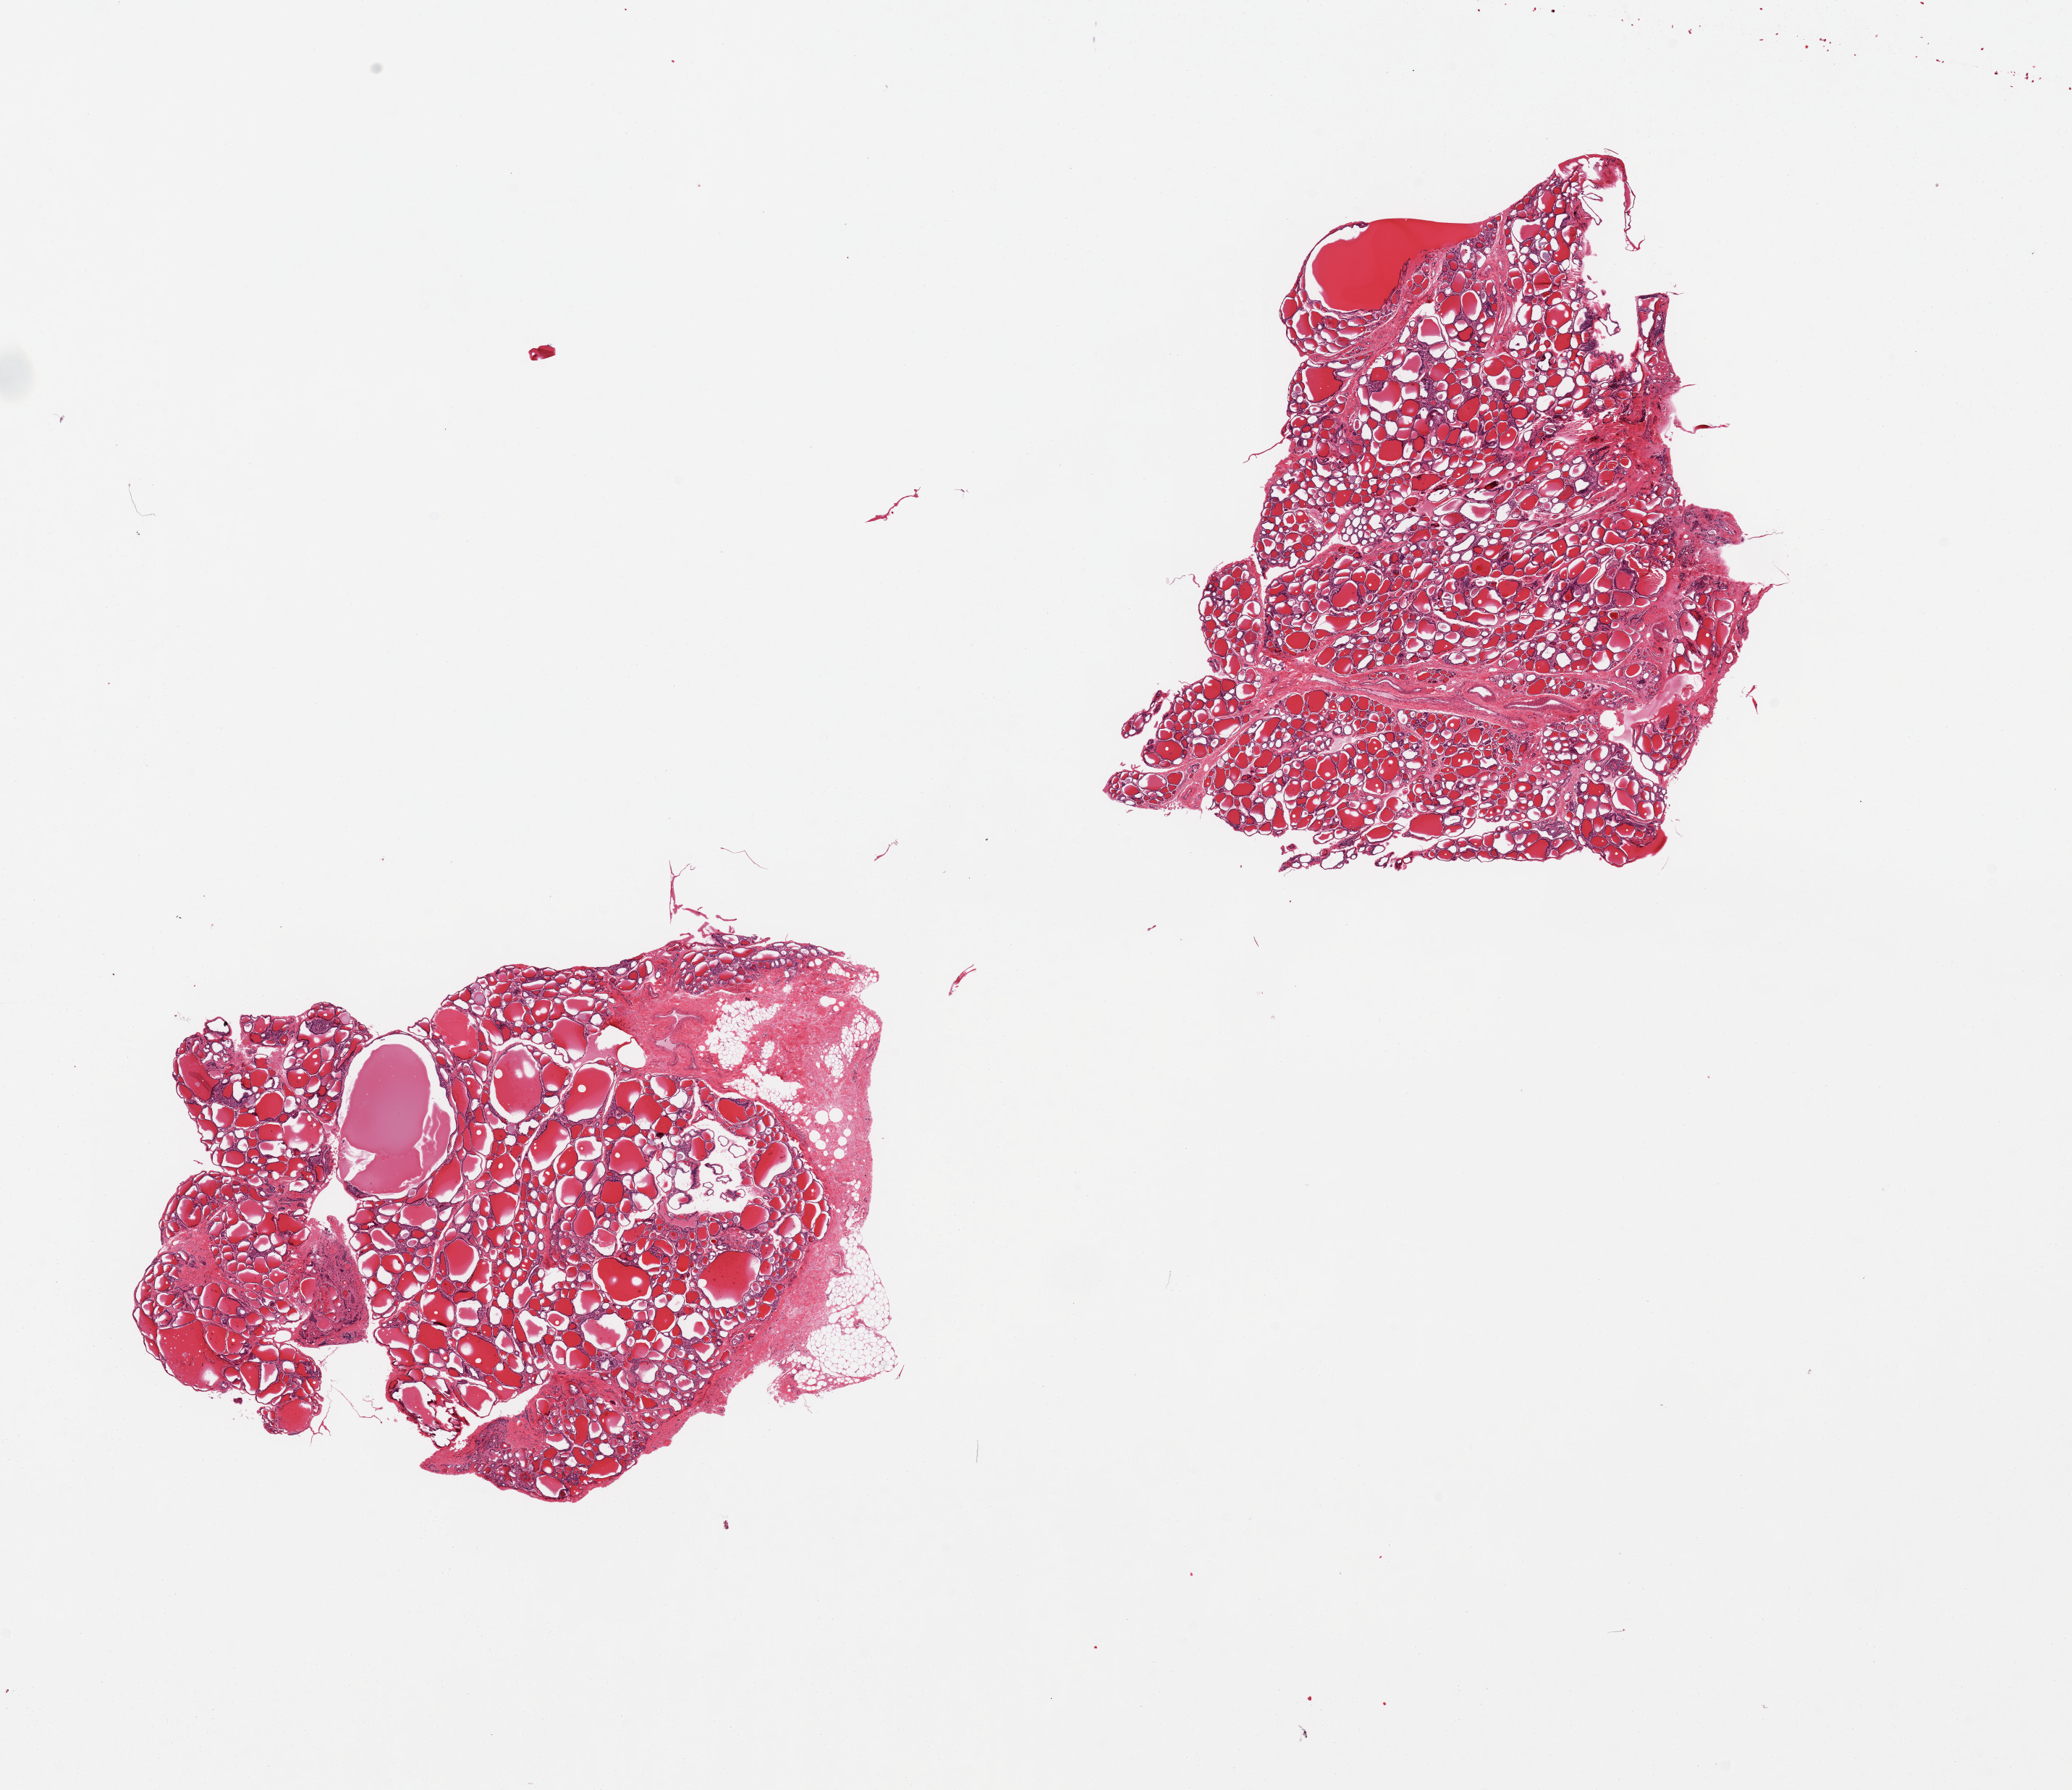
Whole-slide image, haematoxylin and eosin stain, a low-resolution overview of the entire scanned area, about 22.6 x 19.6 mm, PAXgene-fixed, paraffin-embedded tissue, sampled site (target tissue): thyroid, donor tissue sample. Donor sex: male.
• reviewer comment on this tissue sample: 2 pieces, ~2mm colloid cyst, featurs of goiter, regressive changes